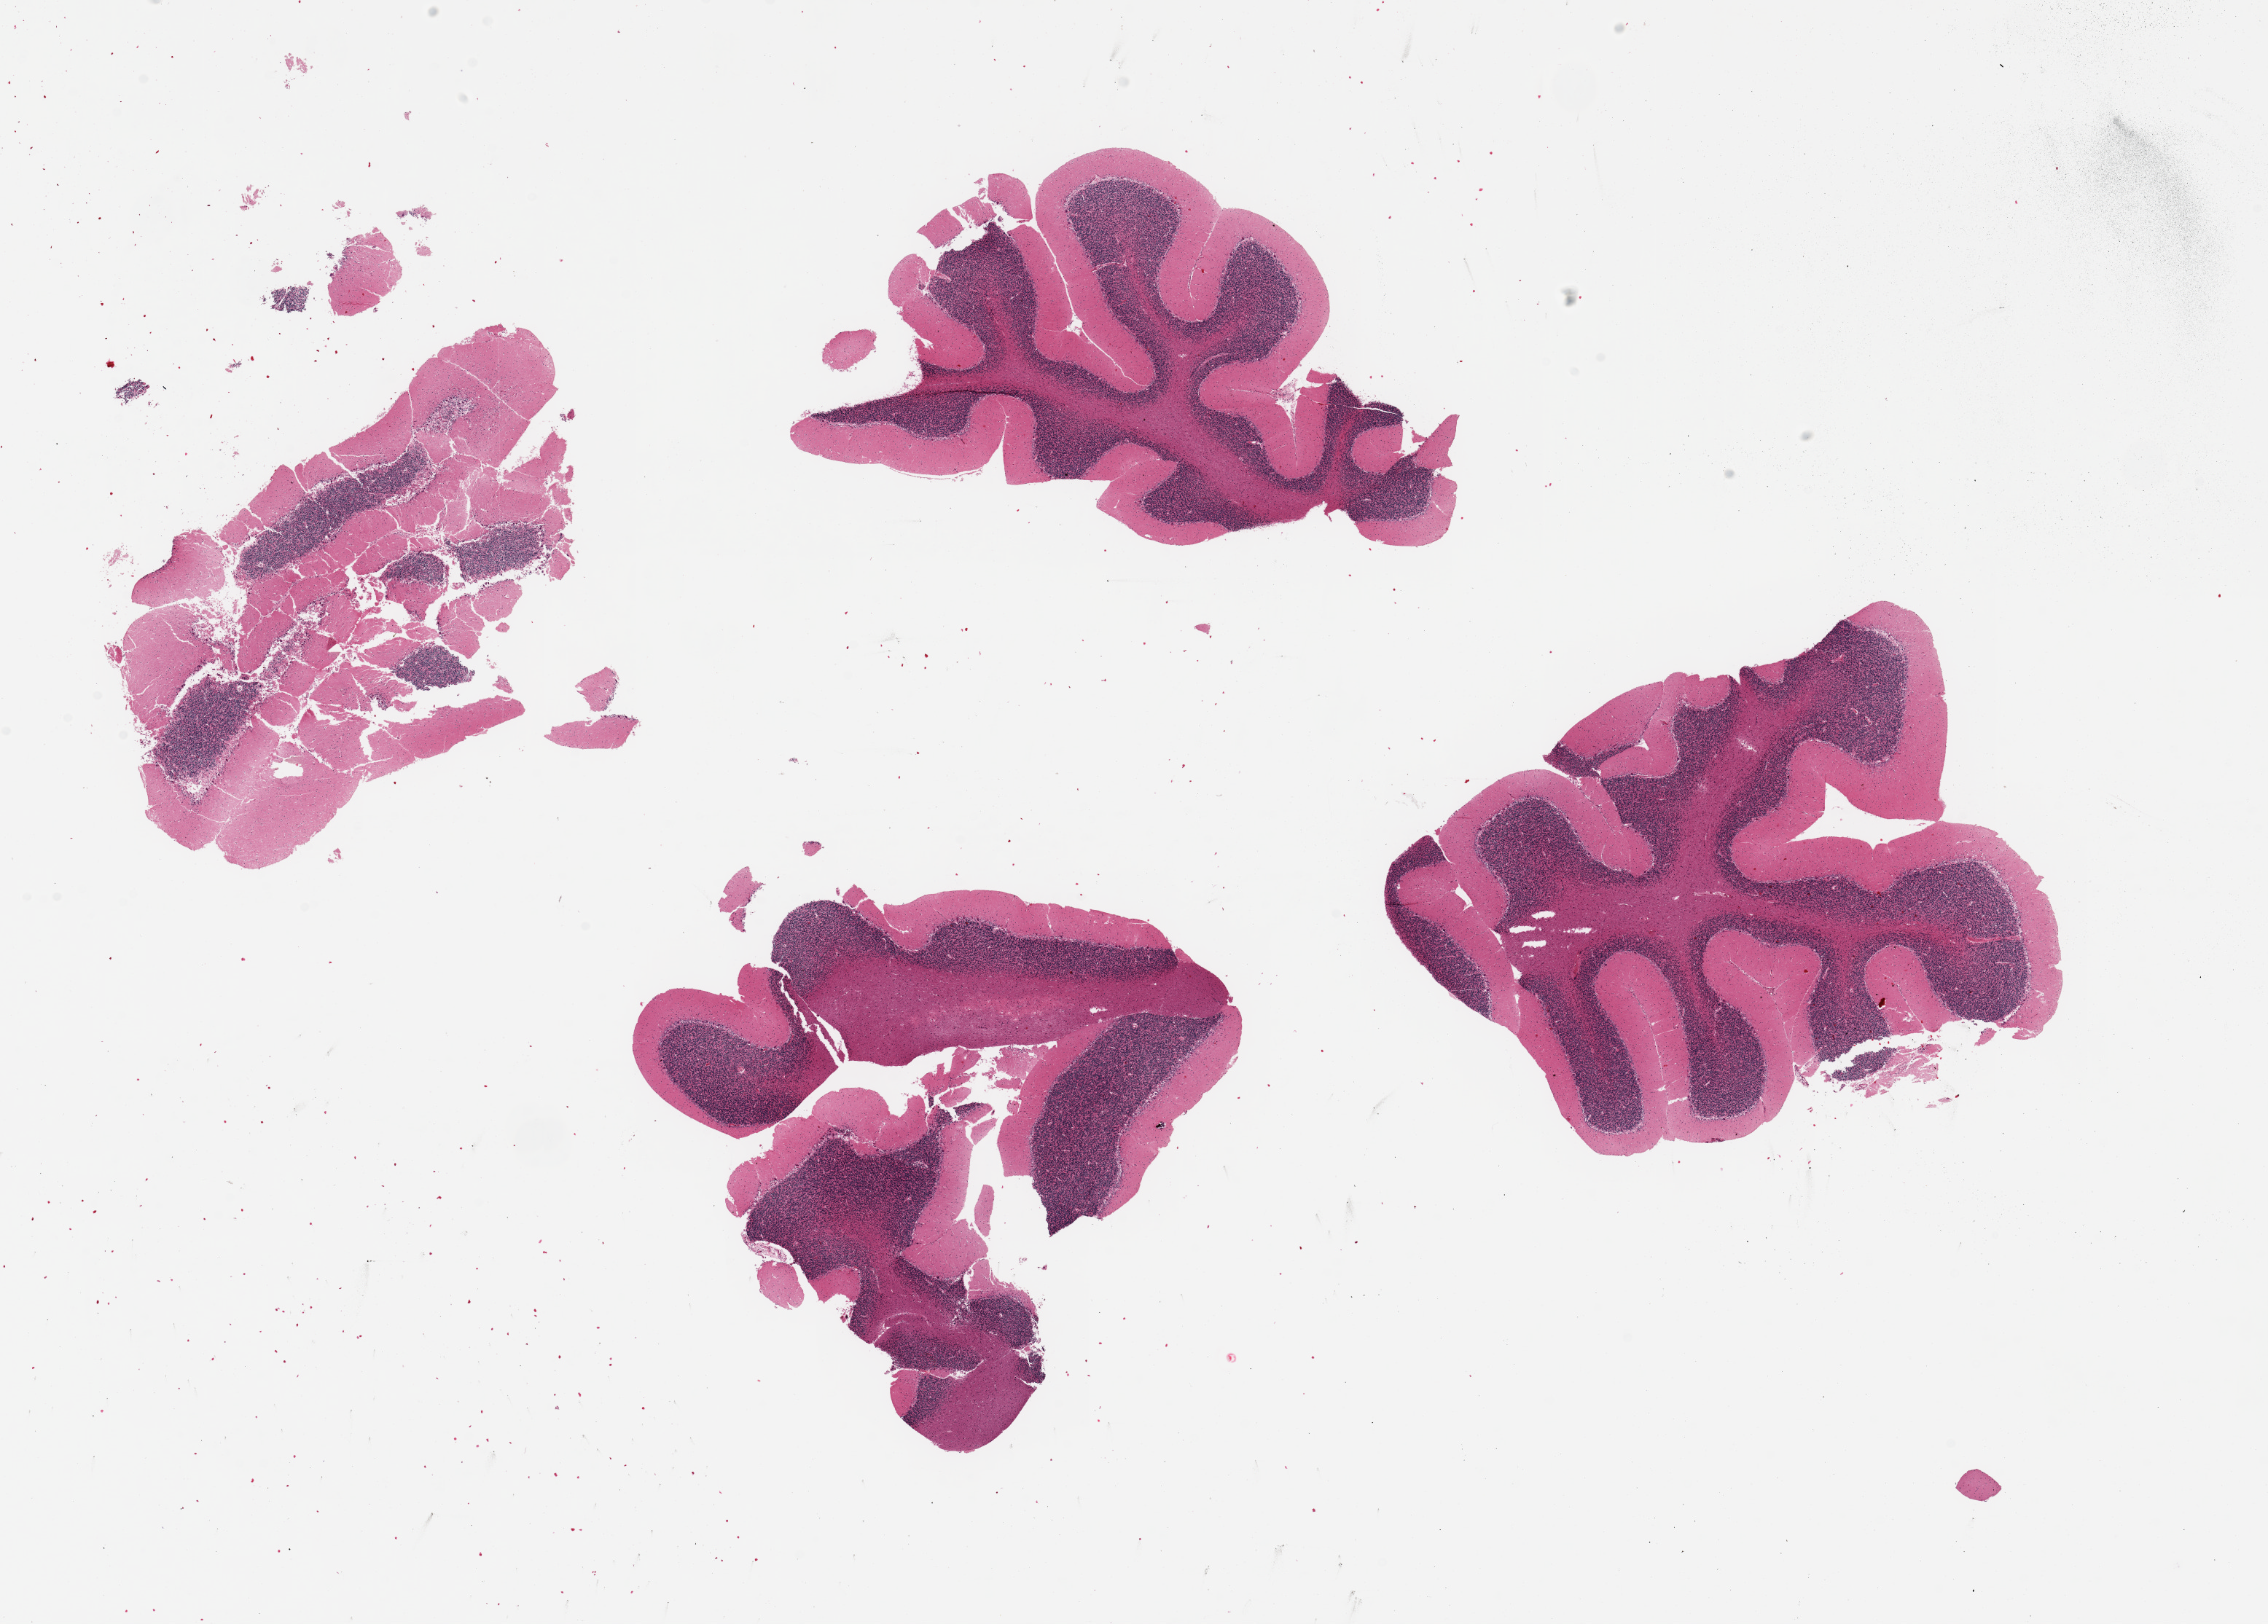
Hematoxylin and eosin (H&E) whole-slide image, whole scanned area (about 24.6 x 17.6 mm) shown as a low-resolution overview. PAXgene-fixed, paraffin-embedded tissue. Section of cerebellum (target tissue). Tissue donor sample. Donor sex: male.
Reviewer comment on this tissue sample: 4 ~6x5mm aliquots.